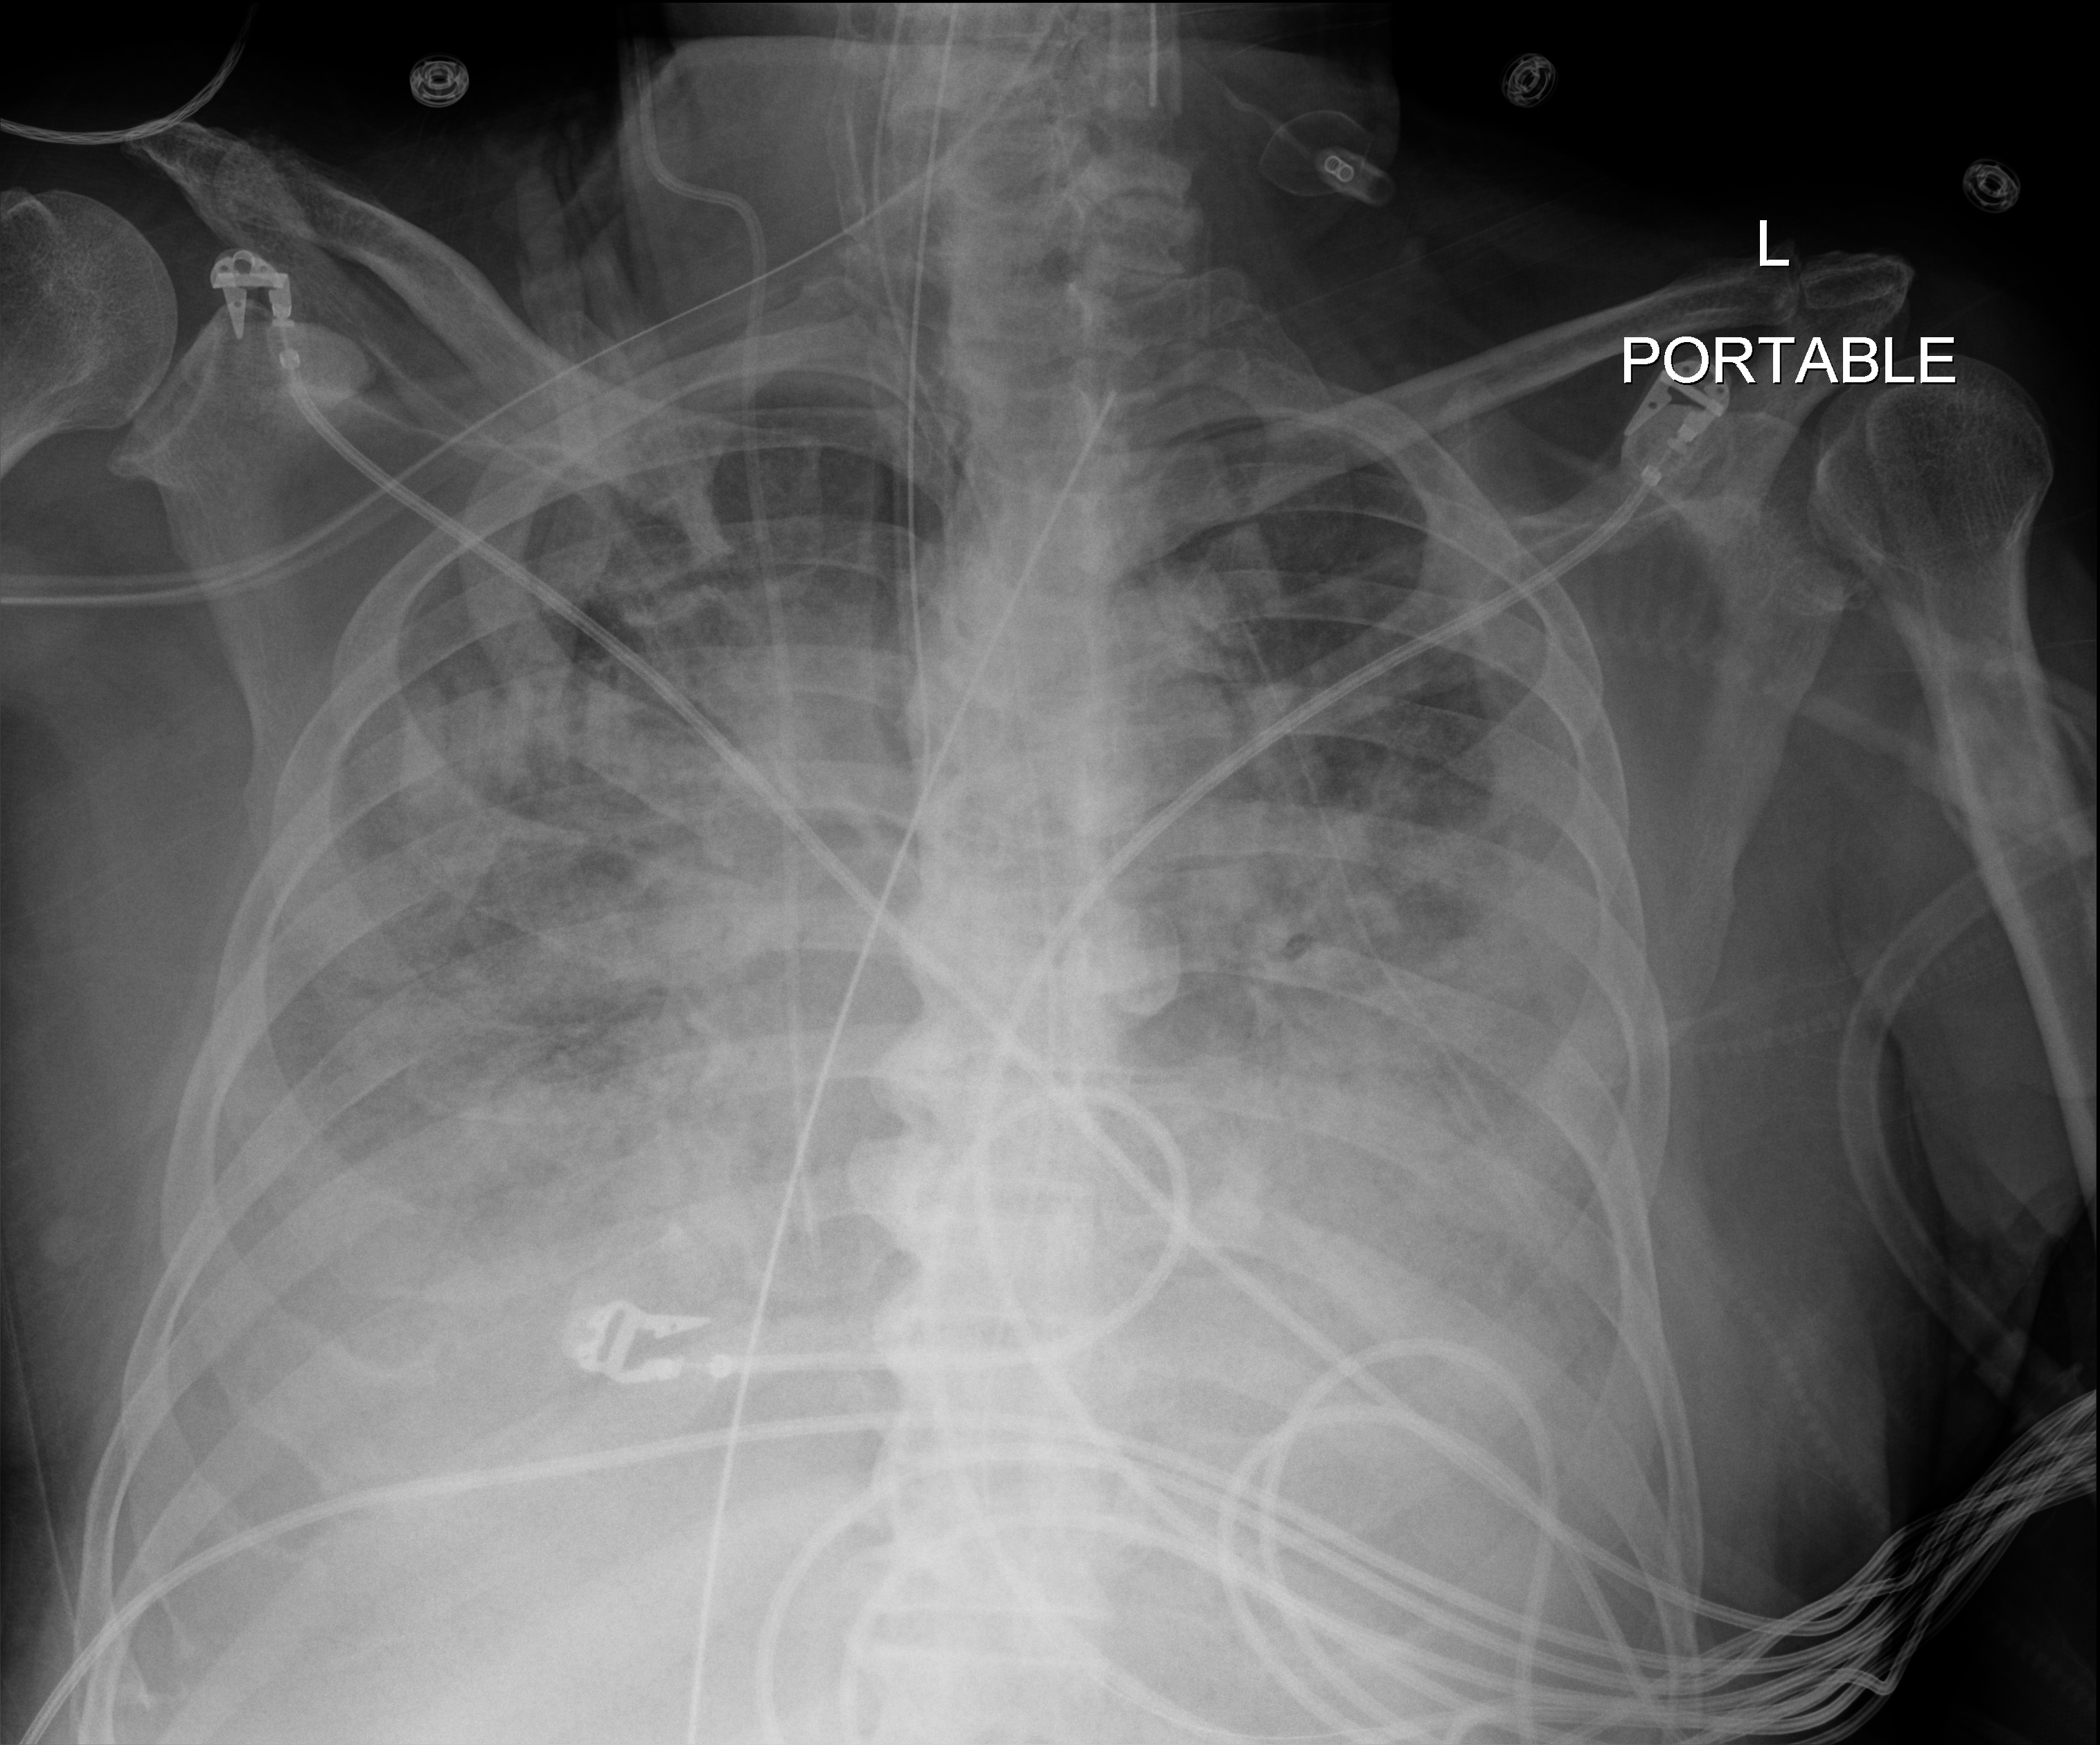
Portable chest radiograph; anteroposterior (AP) projection. Patient hospitalised with COVID-19; male, aged 75–90 years.
Hospital-stay facts (about this admission, not read from this image; timing relative to this image not recorded): mechanically ventilated during this hospital stay: yes; other chronic lung disease (admission record): no.